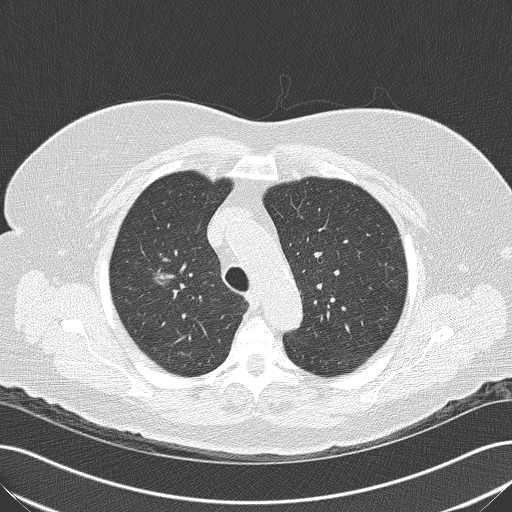
Axial slice from a low-dose chest CT screening exam. Baseline screening round. Lung window (W 1500 / L -600 HU). Lung (sharp) reconstruction kernel (B50f). Slice 137 of 167 in the series. 512 × 512 image matrix. Female, age 74 years at enrolment. Former smoker at enrolment.
Lesion marked by an expert reader, bounding box [x1, y1, x2, y2] px = [137, 253, 195, 315]. The screening reader recorded 2 non-calcified nodules or masses ≥4 mm on this exam; which of them this box marks is not recorded.